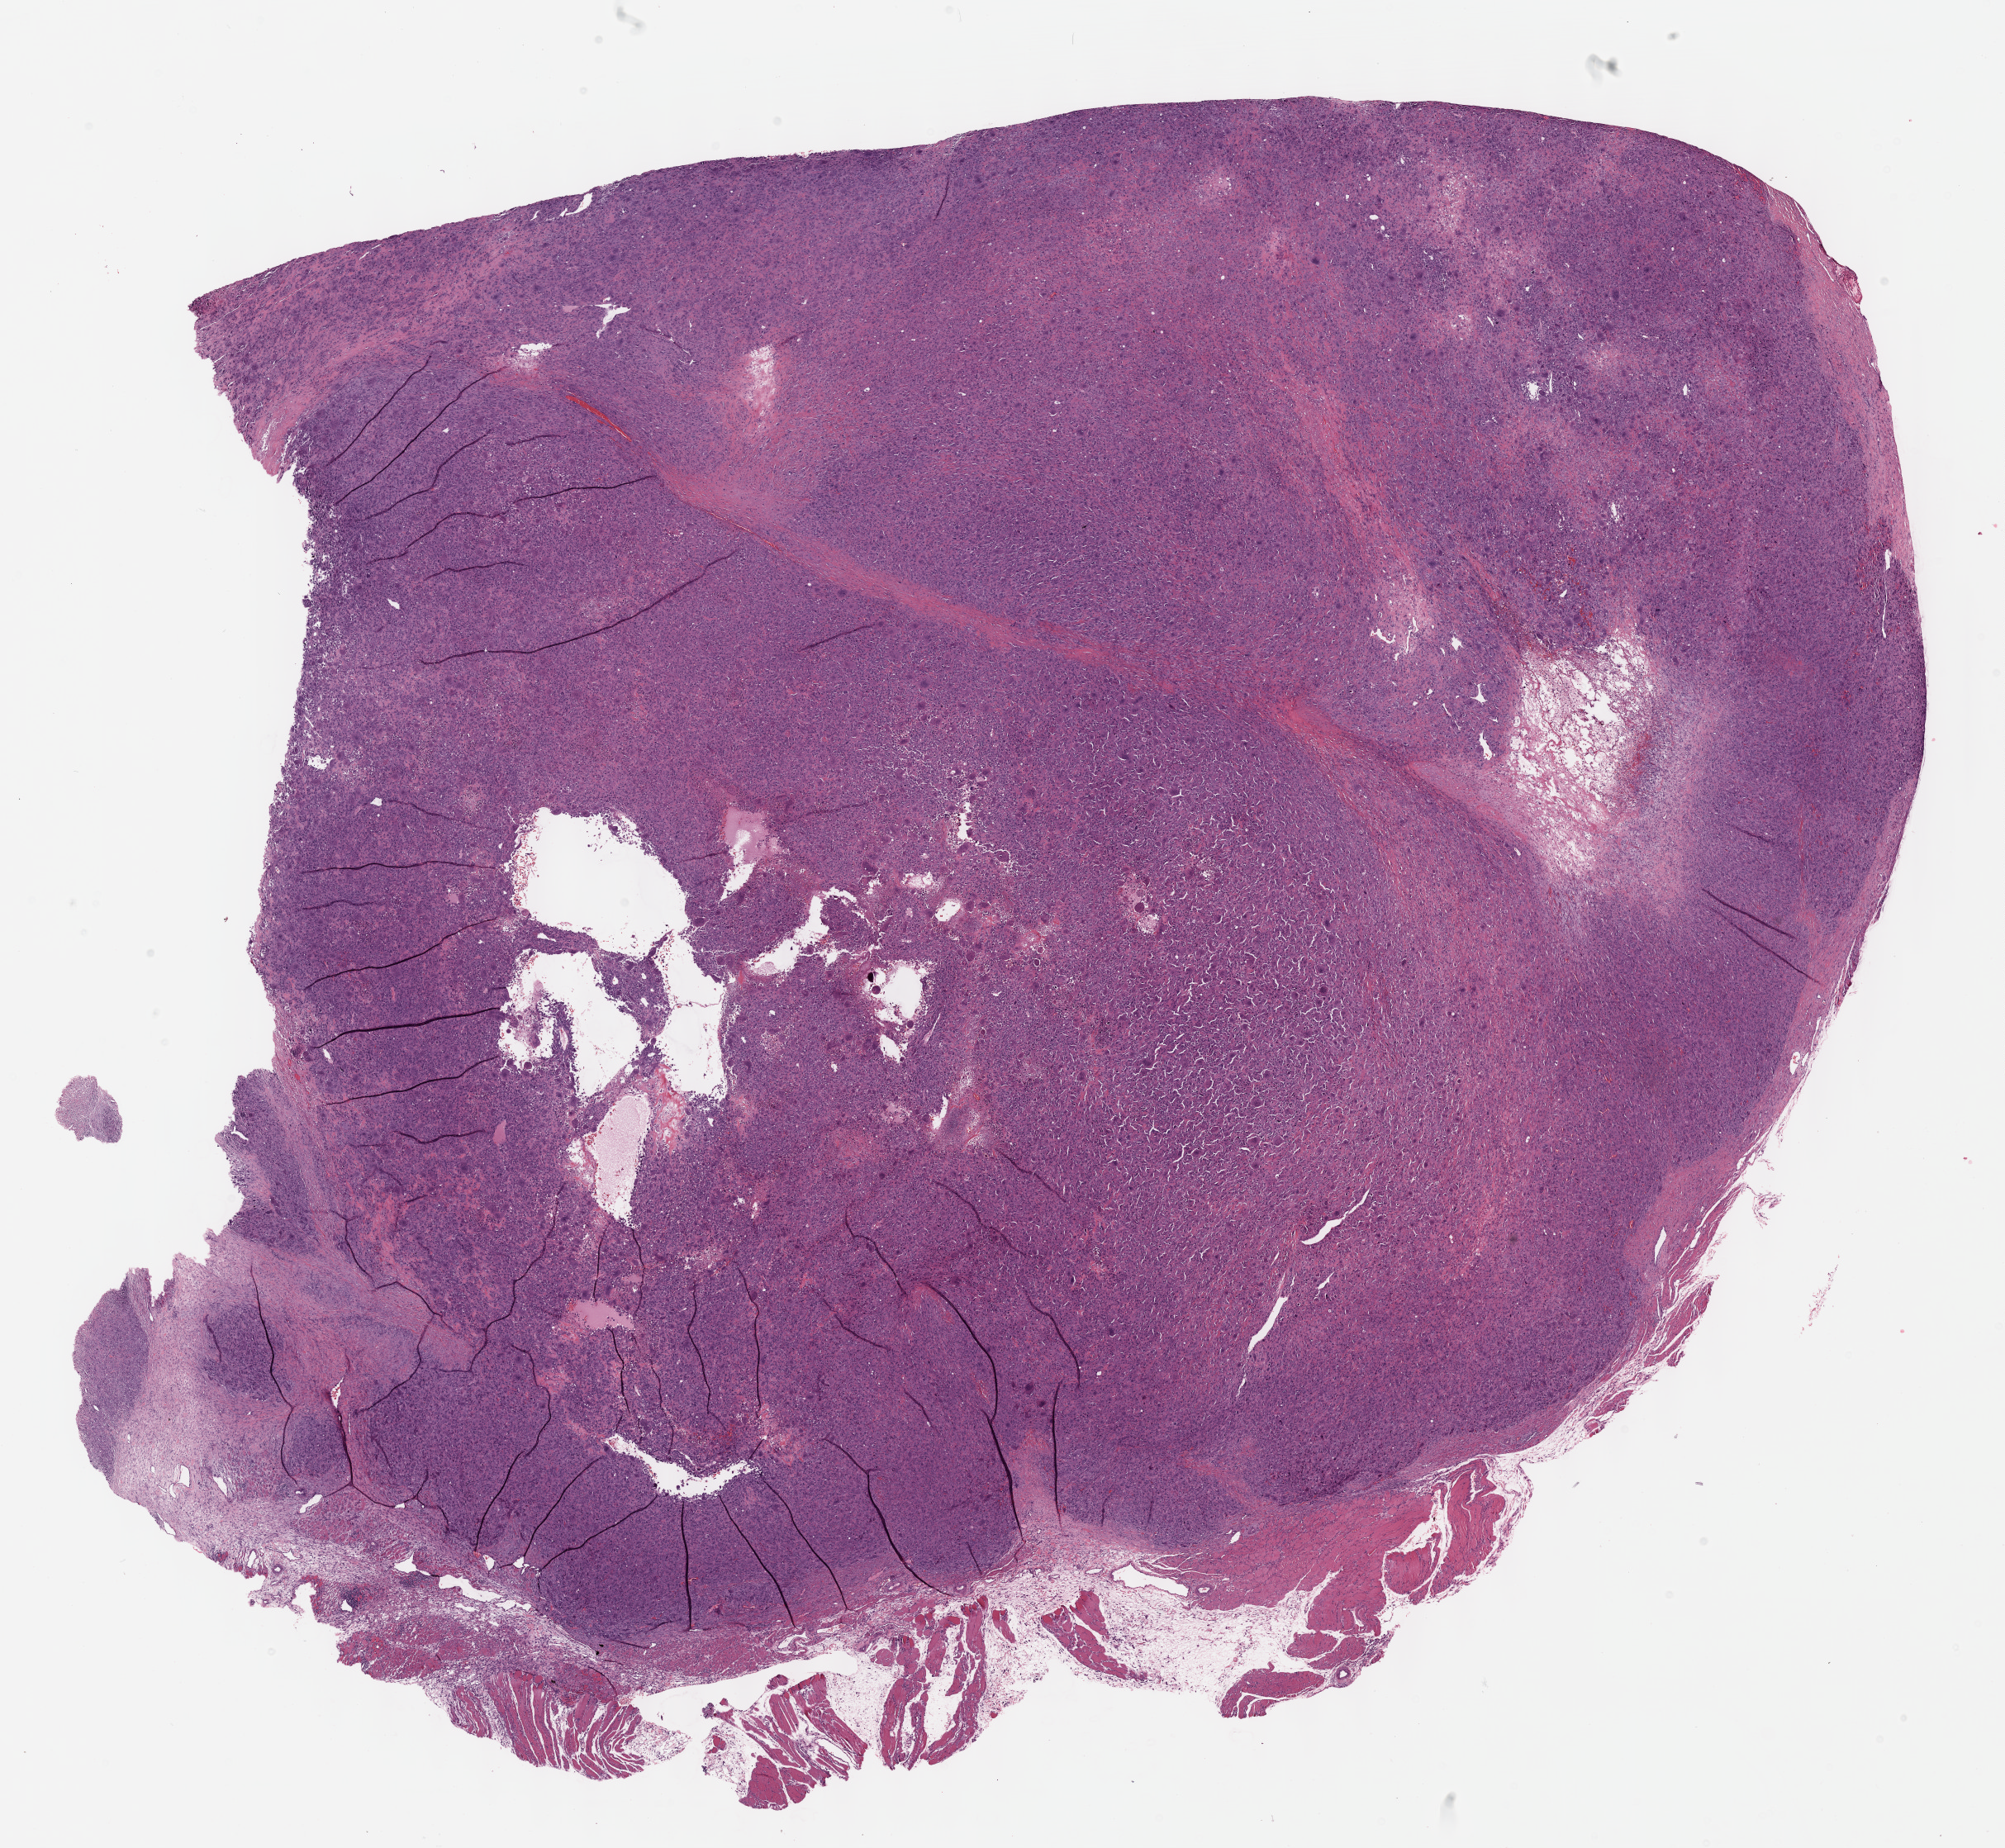
H&E whole-slide image, shown as a low-resolution overview of the whole scanned area (about 19.6 x 18.1 mm, slide scanned at 40x); formalin-fixed paraffin-embedded (FFPE) diagnostic section; primary tumour sample from the connective, subcutaneous and other soft tissues. Female patient.
• pathologic diagnosis: Undifferentiated sarcoma (connective, subcutaneous and other soft tissues of lower limb and hip)